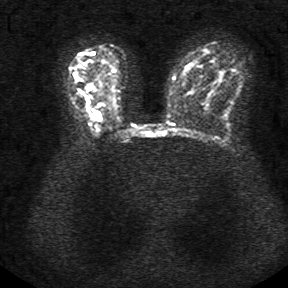
Breast MRI, one axial slice. Position 22 of 34 along the scan axis. Diffusion-weighted series; image 2 of 4 stored at this slice position (different b-values; order by instance number). 1.5 T. 5 mm slice thickness. 288 × 288 image matrix, field of view 340 × 340 mm. Female patient.
Structures marked on this image (expert manual segmentation):
- tumour on diffusion-weighted imaging: bounding box (x1, y1, x2, y2) in pixels: (85, 84, 101, 118)